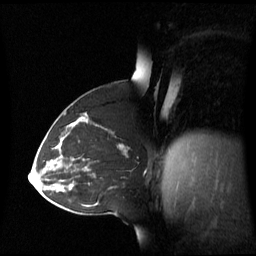
Breast MRI (dynamic contrast-enhanced), one sagittal slice; position 33 of 60 along the scan axis; dynamic contrast-enhanced series, image 2 of 3 at this slice position (ordered by acquisition); 1.5 T; TE 4.2 ms, TR 8.4 ms; 256 × 256 image matrix. Patient: female, 43 years. From the clinical record (not read from this slice): setting: breast cancer imaged before/during neoadjuvant chemotherapy; receptor status: triple-negative.
Outlined on this slice (semi-automatically segmented with operator editing):
- analysis volume of interest (the breast-tissue region the enhancement analysis was run in; not a lesion): bounding box (x1, y1, x2, y2) in pixels: (55, 124, 139, 173)
- tumour enhancement mask (voxels above the 70 % enhancement threshold inside the analysis volume of interest): (120, 144, 124, 148)